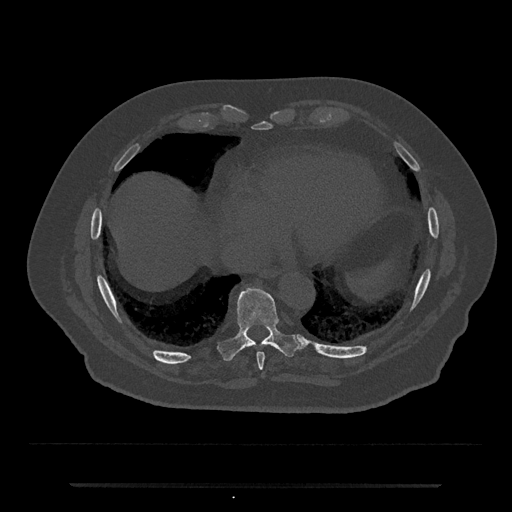
CT including the spine, one axial slice. Position 768 of 797 along the scan axis. Bone window (W 1800 / L 400 HU). 0.5 mm slice thickness. 512 × 512 image matrix, field of view 434 × 434 mm. Male patient, age 80 years. From the clinical record (not read from this slice): primary cancer: prostate; vertebrae with lytic lesions (as recorded): L1, T11.
Annotated regions visible in this slice (semi-automatic segmentation, software-assisted and operator-edited):
- T8 vertebra: bounding box <257,352,265,372> (left, top, right, bottom; pixels)
- T9 vertebra: <219,286,303,361>